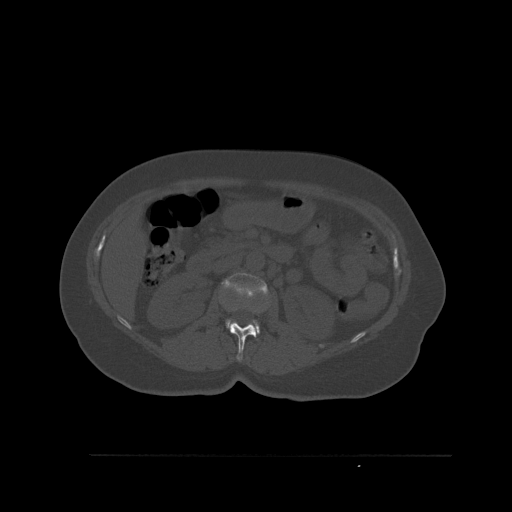
CT including the spine, one axial slice; position 258 of 527 along the scan axis; bone window (W 1800 / L 400 HU); 1.5 mm slice thickness; 512 × 512 image matrix, field of view 470 × 470 mm. Female patient, age 73 years. From the clinical record (not read from this slice): primary cancer: breast.
Outlined on this slice (semi-automatic segmentation, software-assisted and operator-edited):
- L1 vertebra: bounding box [x1, y1, x2, y2] px = [228, 307, 258, 361]
- L2 vertebra: [225, 273, 267, 334]